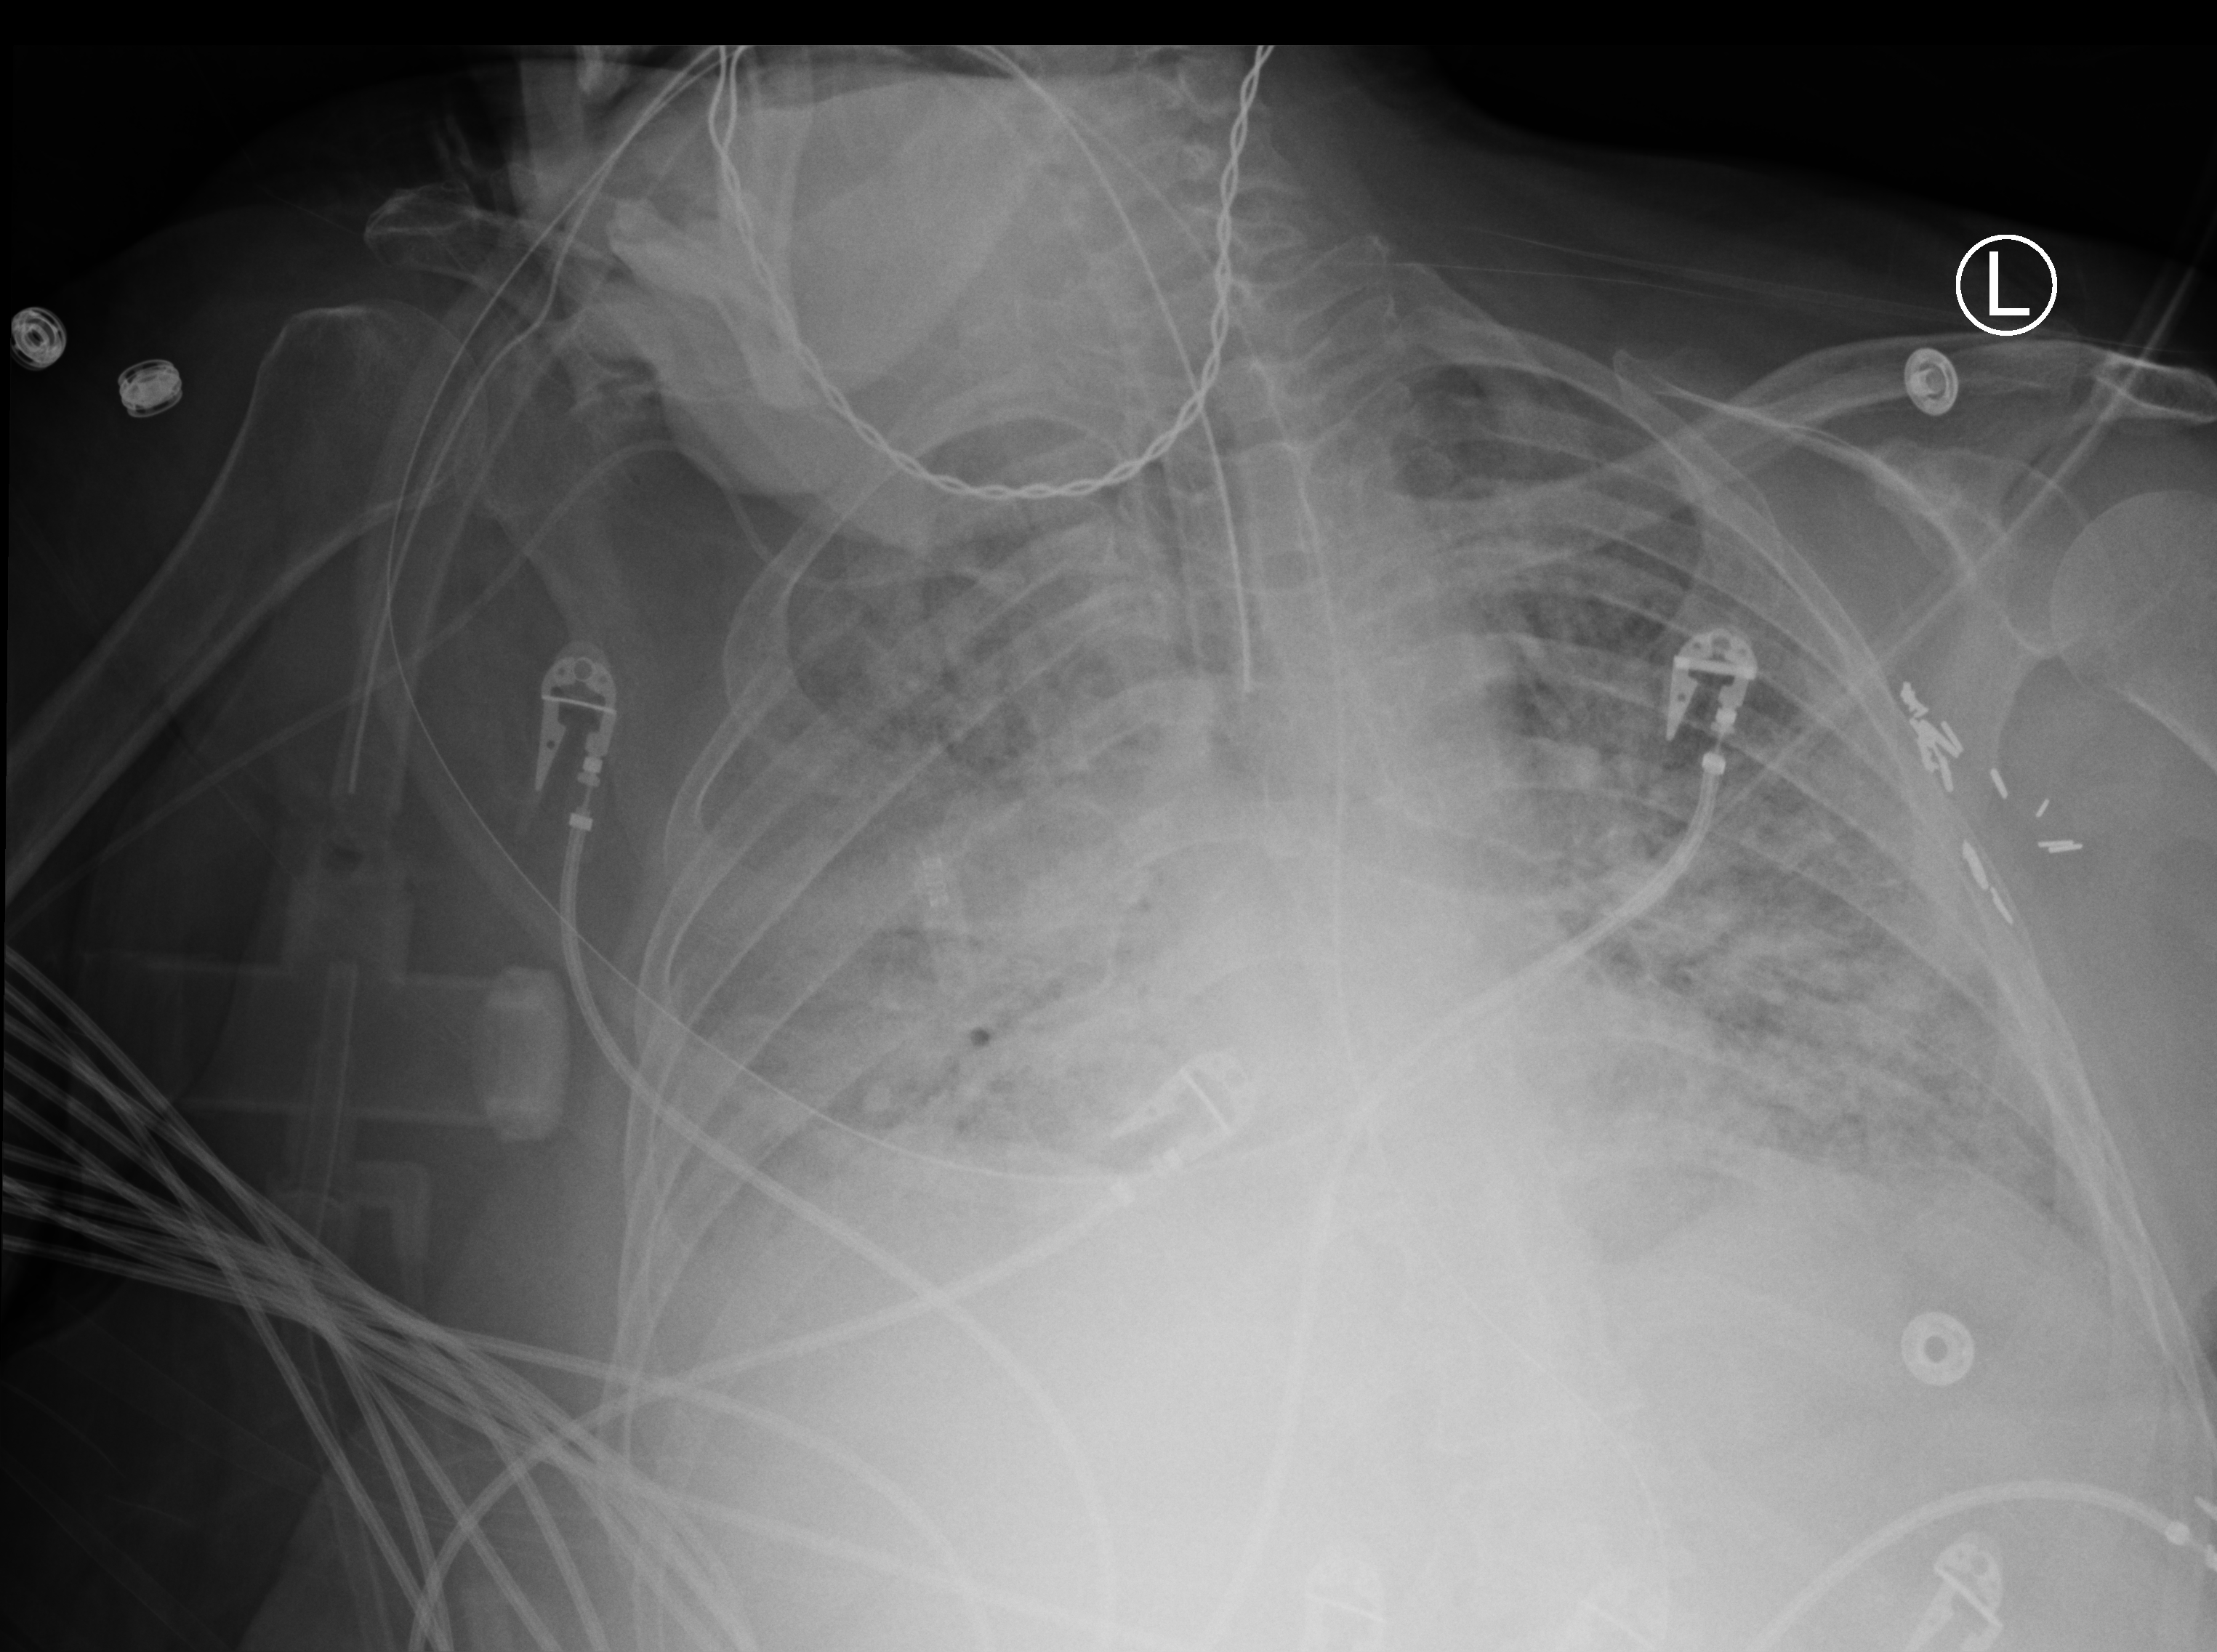
Portable chest radiograph, anteroposterior (AP) projection. Patient hospitalised with COVID-19; female, aged 60–74 years.
Hospital-stay facts (about this admission, not read from this image; timing relative to this image not recorded): smoking status (admission record): never; admitted to intensive care during this hospital stay: yes; mechanically ventilated during this hospital stay: yes.